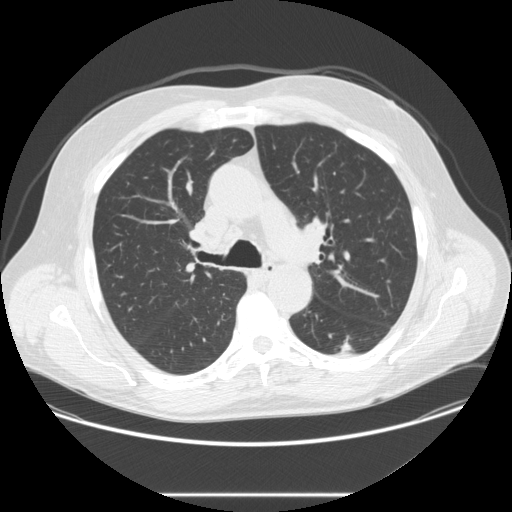
Low-dose screening chest CT, one axial slice; reconstruction kernel STANDARD; 120 kVp; lung window (W 1500 / L -600 HU); 2.5 mm slice thickness; 512 × 512 image matrix.
Outlined on this slice (manually delineated by an expert):
- lesion 1 (tumor, lower lobe of left lung): bounding box <338,342,354,355> (left, top, right, bottom; pixels)